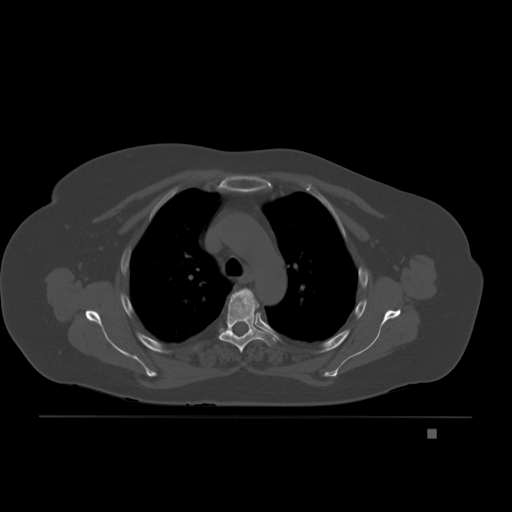
CT including the spine, one axial slice; slice 153 of 221 in the series (ordered by position); bone window (W 1800 / L 400 HU); 3 mm slice thickness; 512 × 512 image matrix. Female patient, age 63 years. Case-level facts recorded for this patient, not image findings: primary cancer: breast.
Outlined on this slice (semi-automatic segmentation, software-assisted and operator-edited):
- T4 vertebra: bounding box <218,289,277,352> (left, top, right, bottom; pixels)